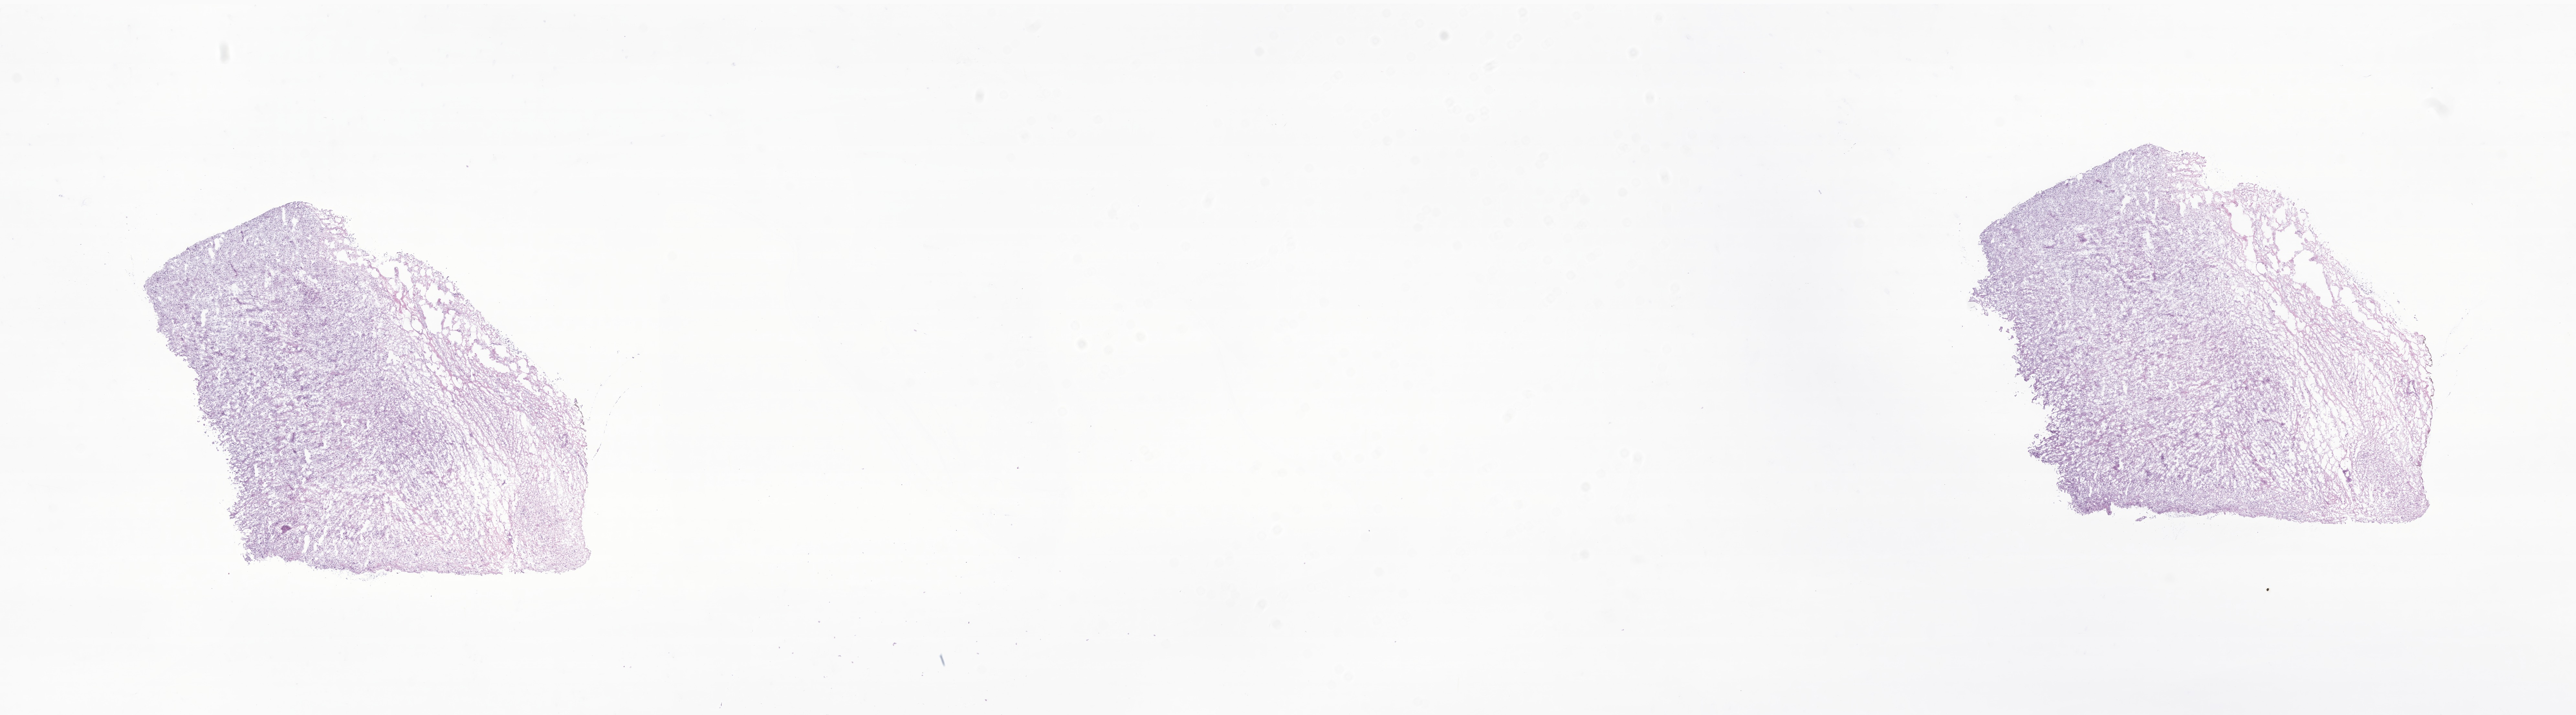
Whole-slide image, haematoxylin and eosin stain of tumor tissue from the mandible, low-resolution overview of the scanned area, about 33.6 x 9.3 mm. Frozen section. Patient: female, age 87 months (7 years 3 months).
Recorded diagnosis: Sarcoma, NOS.